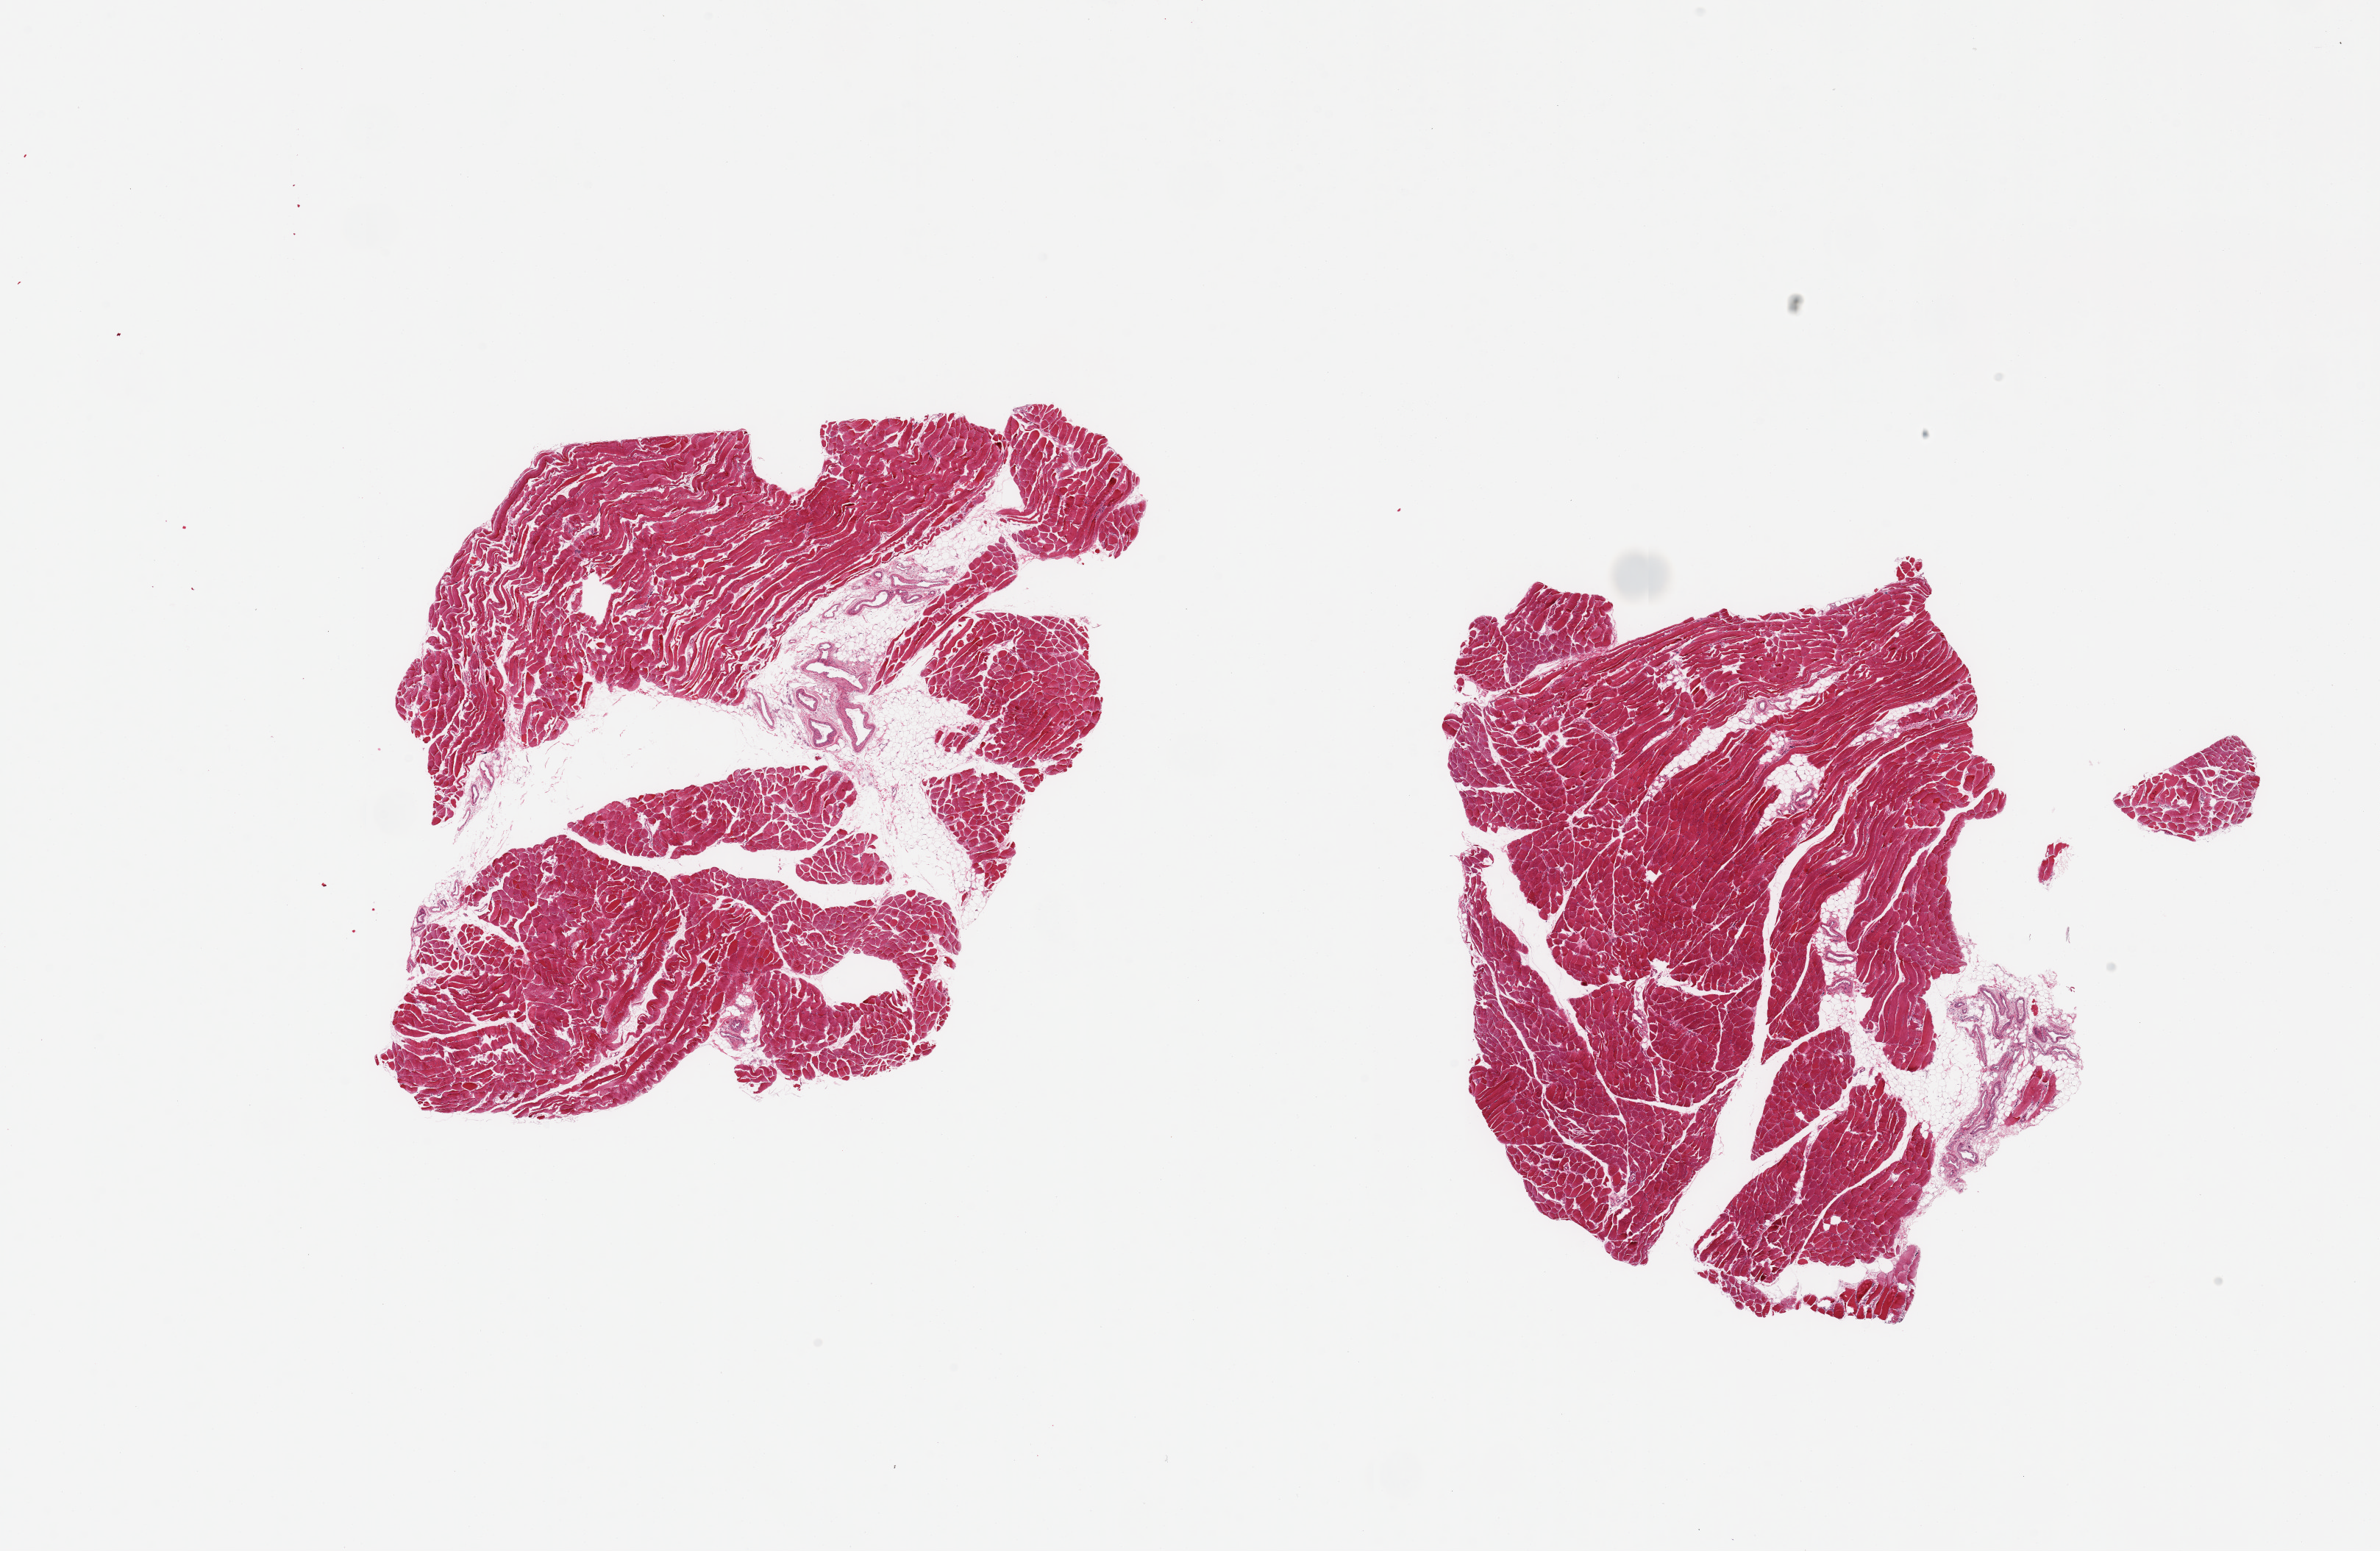
H&E whole-slide image — a low-resolution overview of the entire scanned area, about 25.6 x 16.7 mm; PAXgene-fixed, paraffin-embedded tissue; section of skeletal muscle (target tissue); donor tissue sample. Donor sex: male.
* review note (as recorded): 2 pieces; 10% fat content